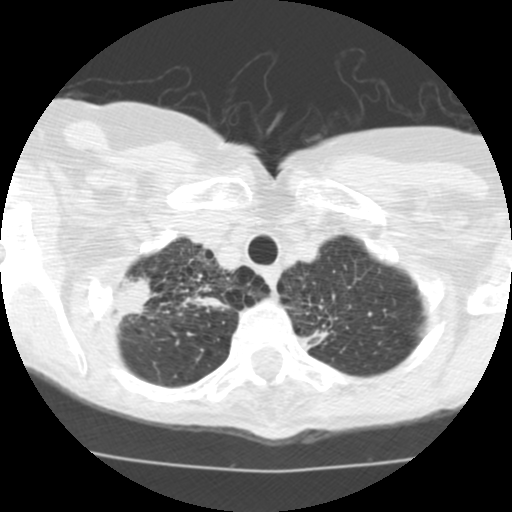
Low-dose screening chest CT, one axial slice; slice 103 of 115 in the series (ordered by position); reconstruction kernel STANDARD; lung window (W 1500 / L -600 HU); 512 × 512 image matrix, field of view 280 × 280 mm.
Structures marked on this image (manually delineated by an expert):
- lesion 1 (tumor, upper lobe of right lung): bounding box <116,277,151,316> (left, top, right, bottom; pixels)